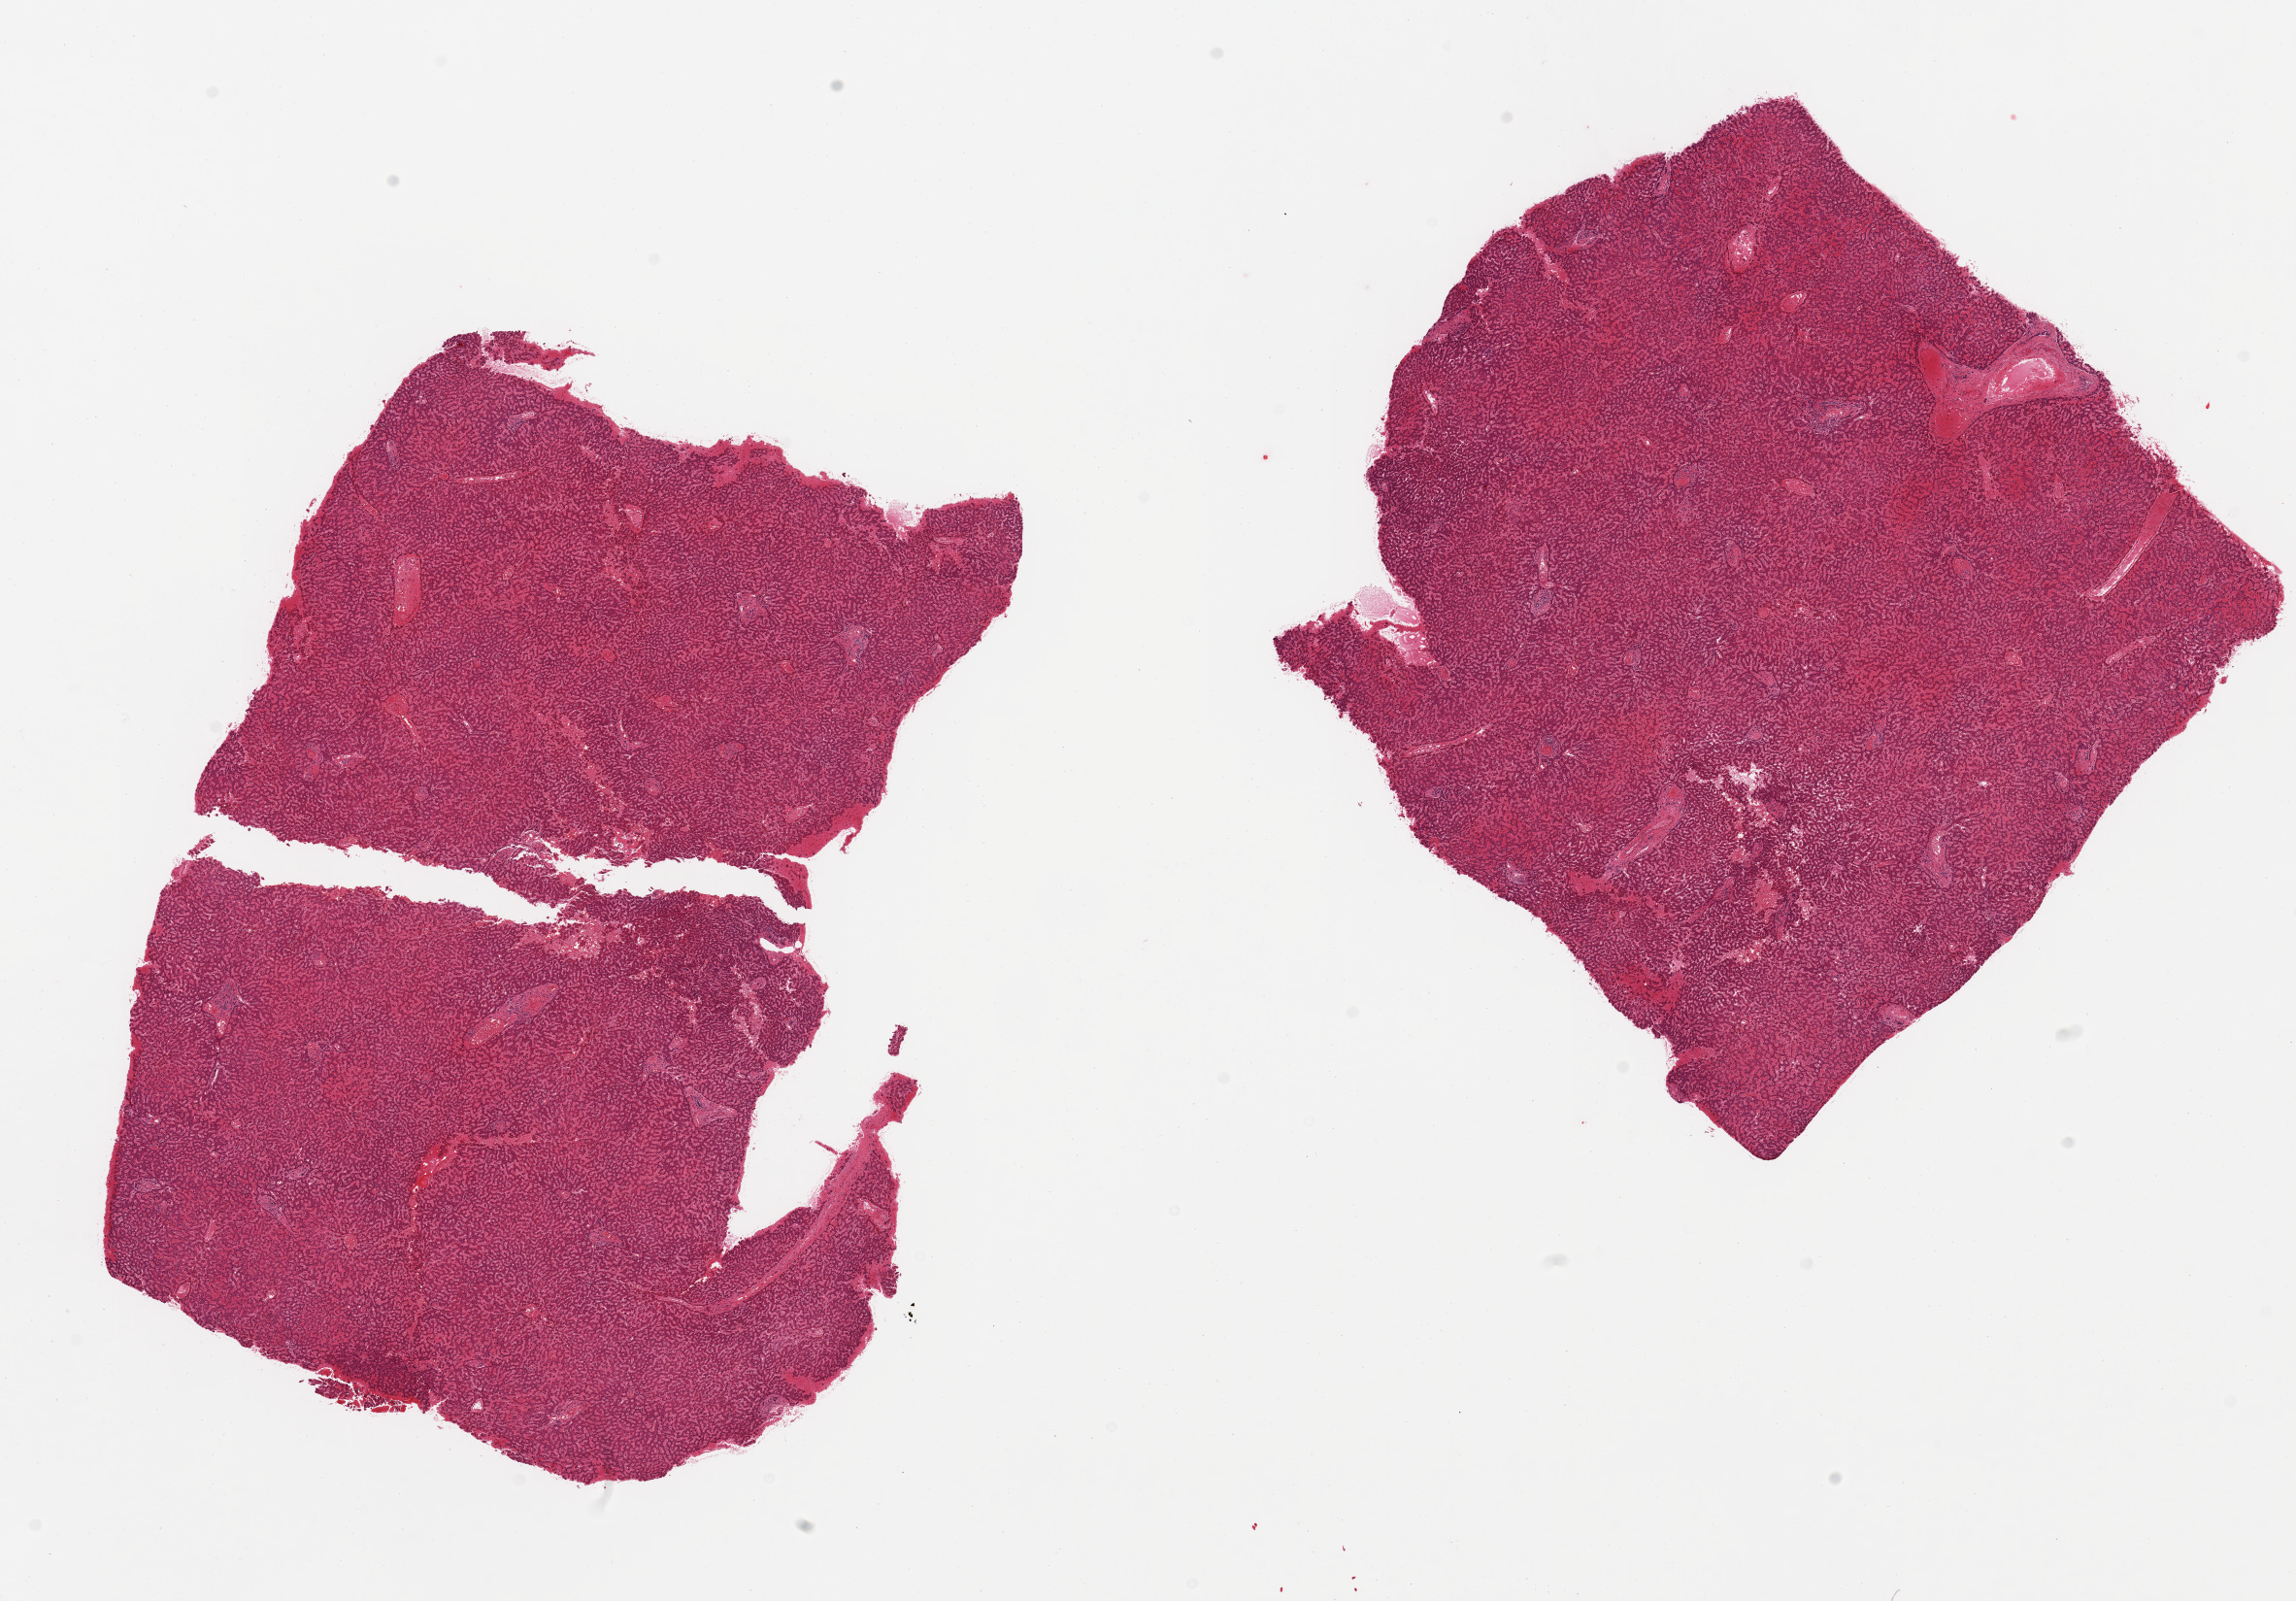
Whole-slide image, hematoxylin and eosin (H&E) stain, whole scanned area (about 18.7 x 13.0 mm) shown as a low-resolution overview. PAXgene-fixed paraffin-embedded (PFPE) section. Target tissue: liver. Donor tissue sample. Male donor.
* review note (as recorded): 2 pieces, mild passive congestion